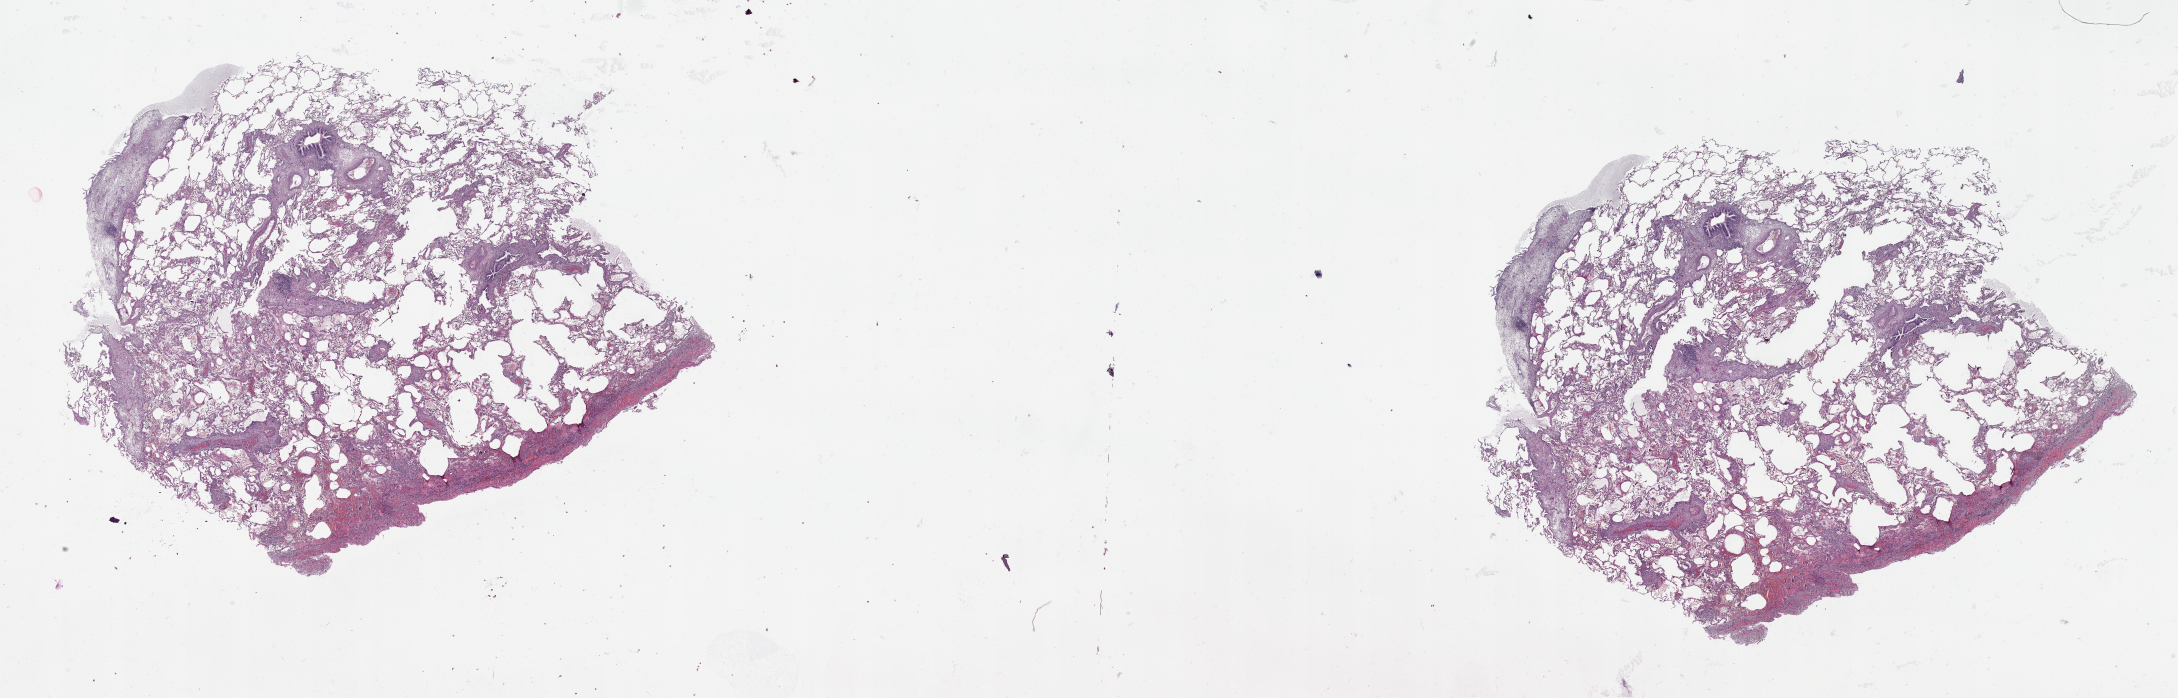
Whole-slide histology image, Hematoxylin and eosin (H&E) stained, low-resolution overview of the scanned area, about 35.1 x 11.2 mm. Normal (non-tumour) tissue sample, lung. 67-year-old male patient.
This section: normal (non-tumour) tissue from the same patient. Patient diagnosis (cohort enrolment): squamous cell carcinoma (lung).